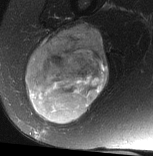
MRI of an extremity soft-tissue mass, one axial slice. Slice 34 of 77 in the series (ordered by position). T2-weighted fat-saturated. MR volume resampled by the dataset authors to the PET/CT grid (not the native acquisition matrix). 153 × 156 image matrix, field of view 149 × 152 mm. Female patient. Case-level facts recorded for this patient, not image findings: histological type: synovial sarcoma; grade: intermediate; site of the primary tumour: right buttock.
Structures marked on this image (expert contour drawn on MRI and transferred to this co-registered scan by the dataset authors):
- gross tumour volume including surrounding oedema: box from (x=26, y=26) to (x=109, y=124) px
- gross tumour volume (mass): (x=26, y=26)–(x=109, y=124)